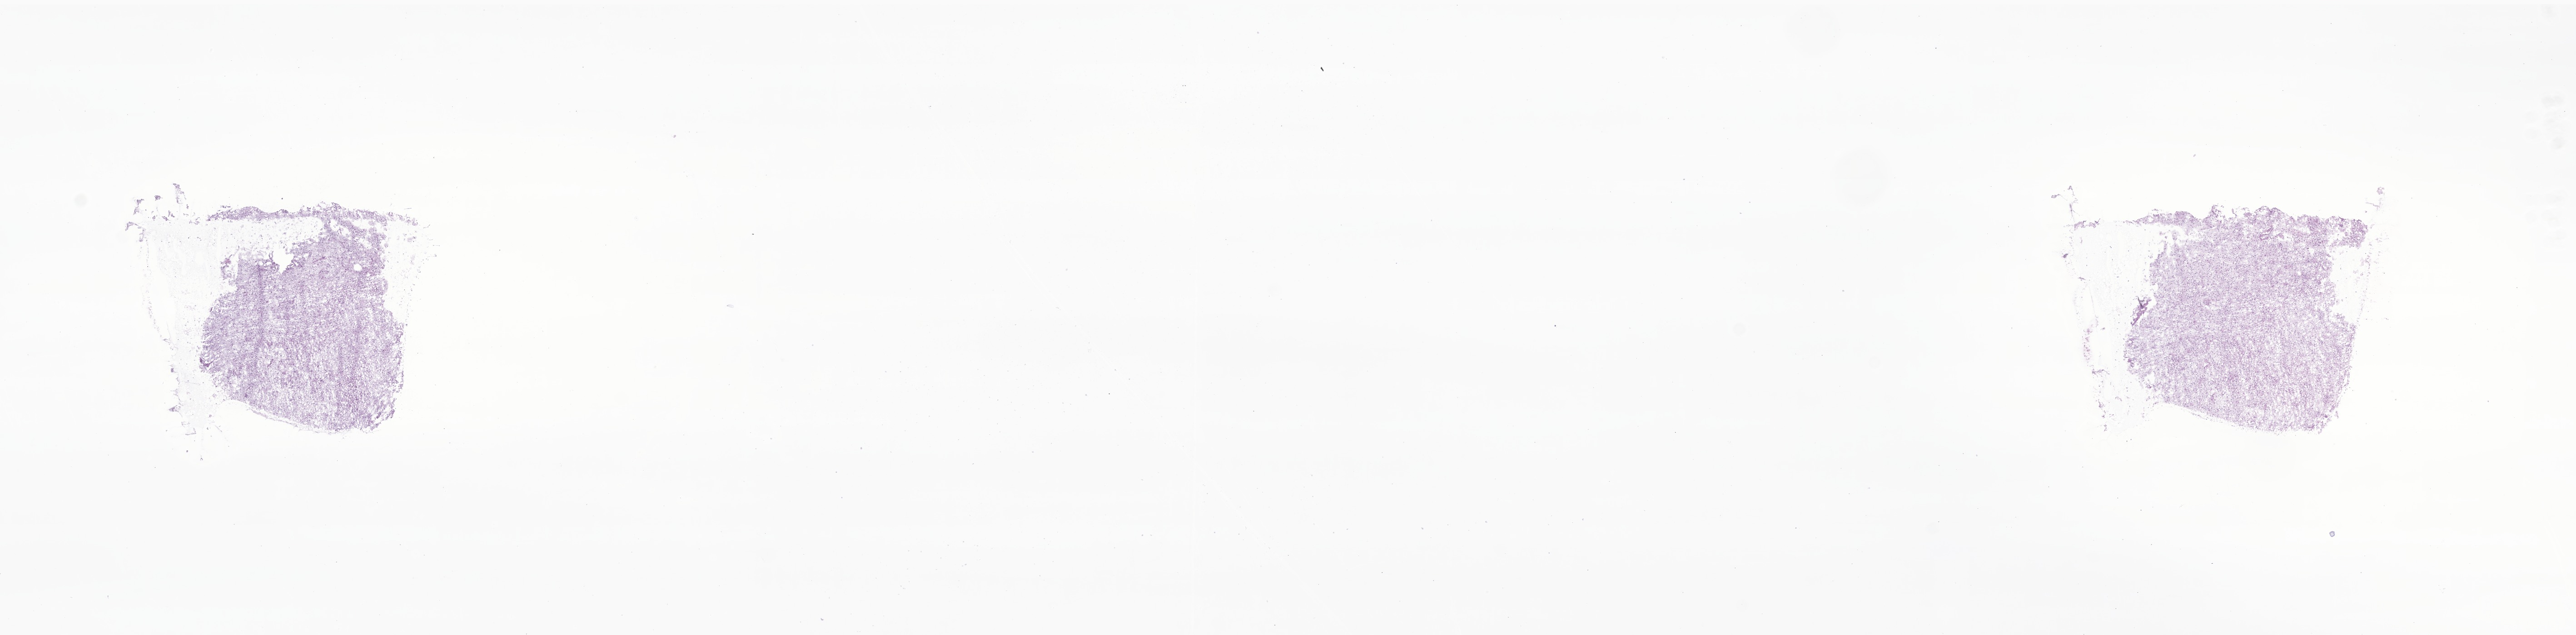
Digitized H&E-stained section of tumor tissue from the brain — a low-resolution overview of the entire scanned area, about 23.9 x 5.9 mm. Cryosection (OCT / tissue freezing medium). Patient male; age 191 months (15 years 11 months).
• diagnosis: Glioma, malignant